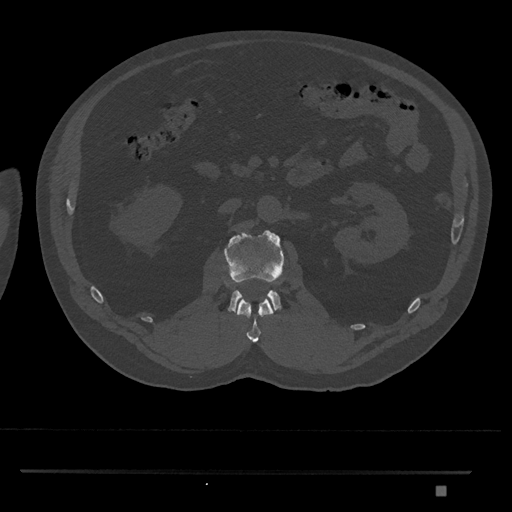
CT including the spine, one axial slice; position 785 of 1134 along the scan axis; reconstruction kernel Br40s/3; 120 kVp; bone window (W 1800 / L 400 HU); 512 × 512 image matrix. Patient: male, 65 years. From the clinical record (not read from this slice): primary cancer: prostate.
Structures marked on this image (semi-automatic segmentation, software-assisted and operator-edited):
- L1 vertebra: bounding box (x1, y1, x2, y2) in pixels: (237, 297, 275, 343)
- L2 vertebra: (224, 230, 286, 312)